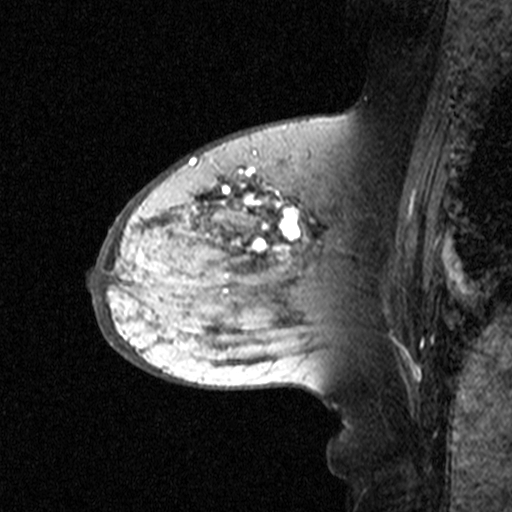
Breast MRI (dynamic contrast-enhanced), one sagittal slice; position 21 of 44 along the scan axis; dynamic contrast-enhanced study with each time point stored as its own series, time point 2 of 3 at this slice position (early post-contrast, ordered by acquisition time); 1.5 T; TE 4.5 ms, TR 11 ms; 3 mm slice thickness; 512 × 512 image matrix. Female patient, age 65 years. Case-level facts recorded for this patient, not image findings: setting: breast cancer imaged before/during neoadjuvant chemotherapy; receptor status: HER2-positive.
Annotated regions visible in this slice (semi-automatic segmentation, software-assisted and operator-edited):
- analysis volume of interest (the breast-tissue region the enhancement analysis was run in; not a lesion): box from (x=160, y=172) to (x=329, y=345) px
- tumour enhancement mask (voxels above the 90 % enhancement threshold inside the analysis volume of interest): (x=186, y=172)–(x=314, y=254)